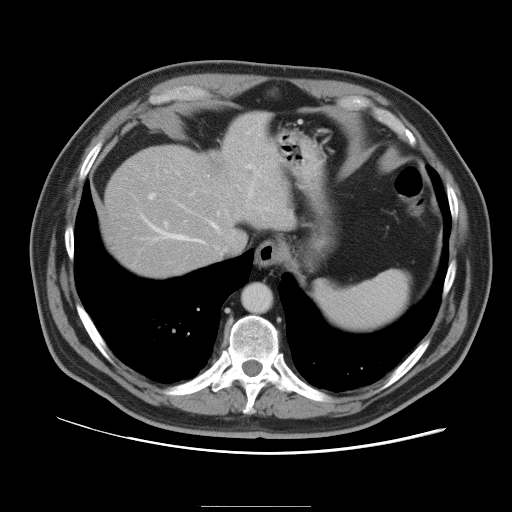
Contrast-enhanced abdominal CT, one axial slice. Slice 83 of 105 in the series (ordered by position). Intravenous contrast given. Soft-tissue window (W 400 / L 40 HU). 5 mm slice thickness. 512 × 512 image matrix, field of view 399 × 399 mm. Male patient, age 64 years. From the clinical record (not read from this slice): diagnosis: colorectal cancer liver metastases, imaged before liver resection; multiple liver metastases: yes; largest metastasis: 3 cm; disease in both lobes: yes.
Structures marked on this image (expert manual segmentation):
- hepatic veins: bounding box (x1, y1, x2, y2) in pixels: (143, 179, 255, 244)
- liver: (105, 113, 289, 275)
- planned liver remnant (the part of the liver to remain after resection): (105, 152, 232, 275)
- portal vein (with intrahepatic branches): (148, 165, 252, 228)
- liver metastasis: (209, 159, 222, 175)